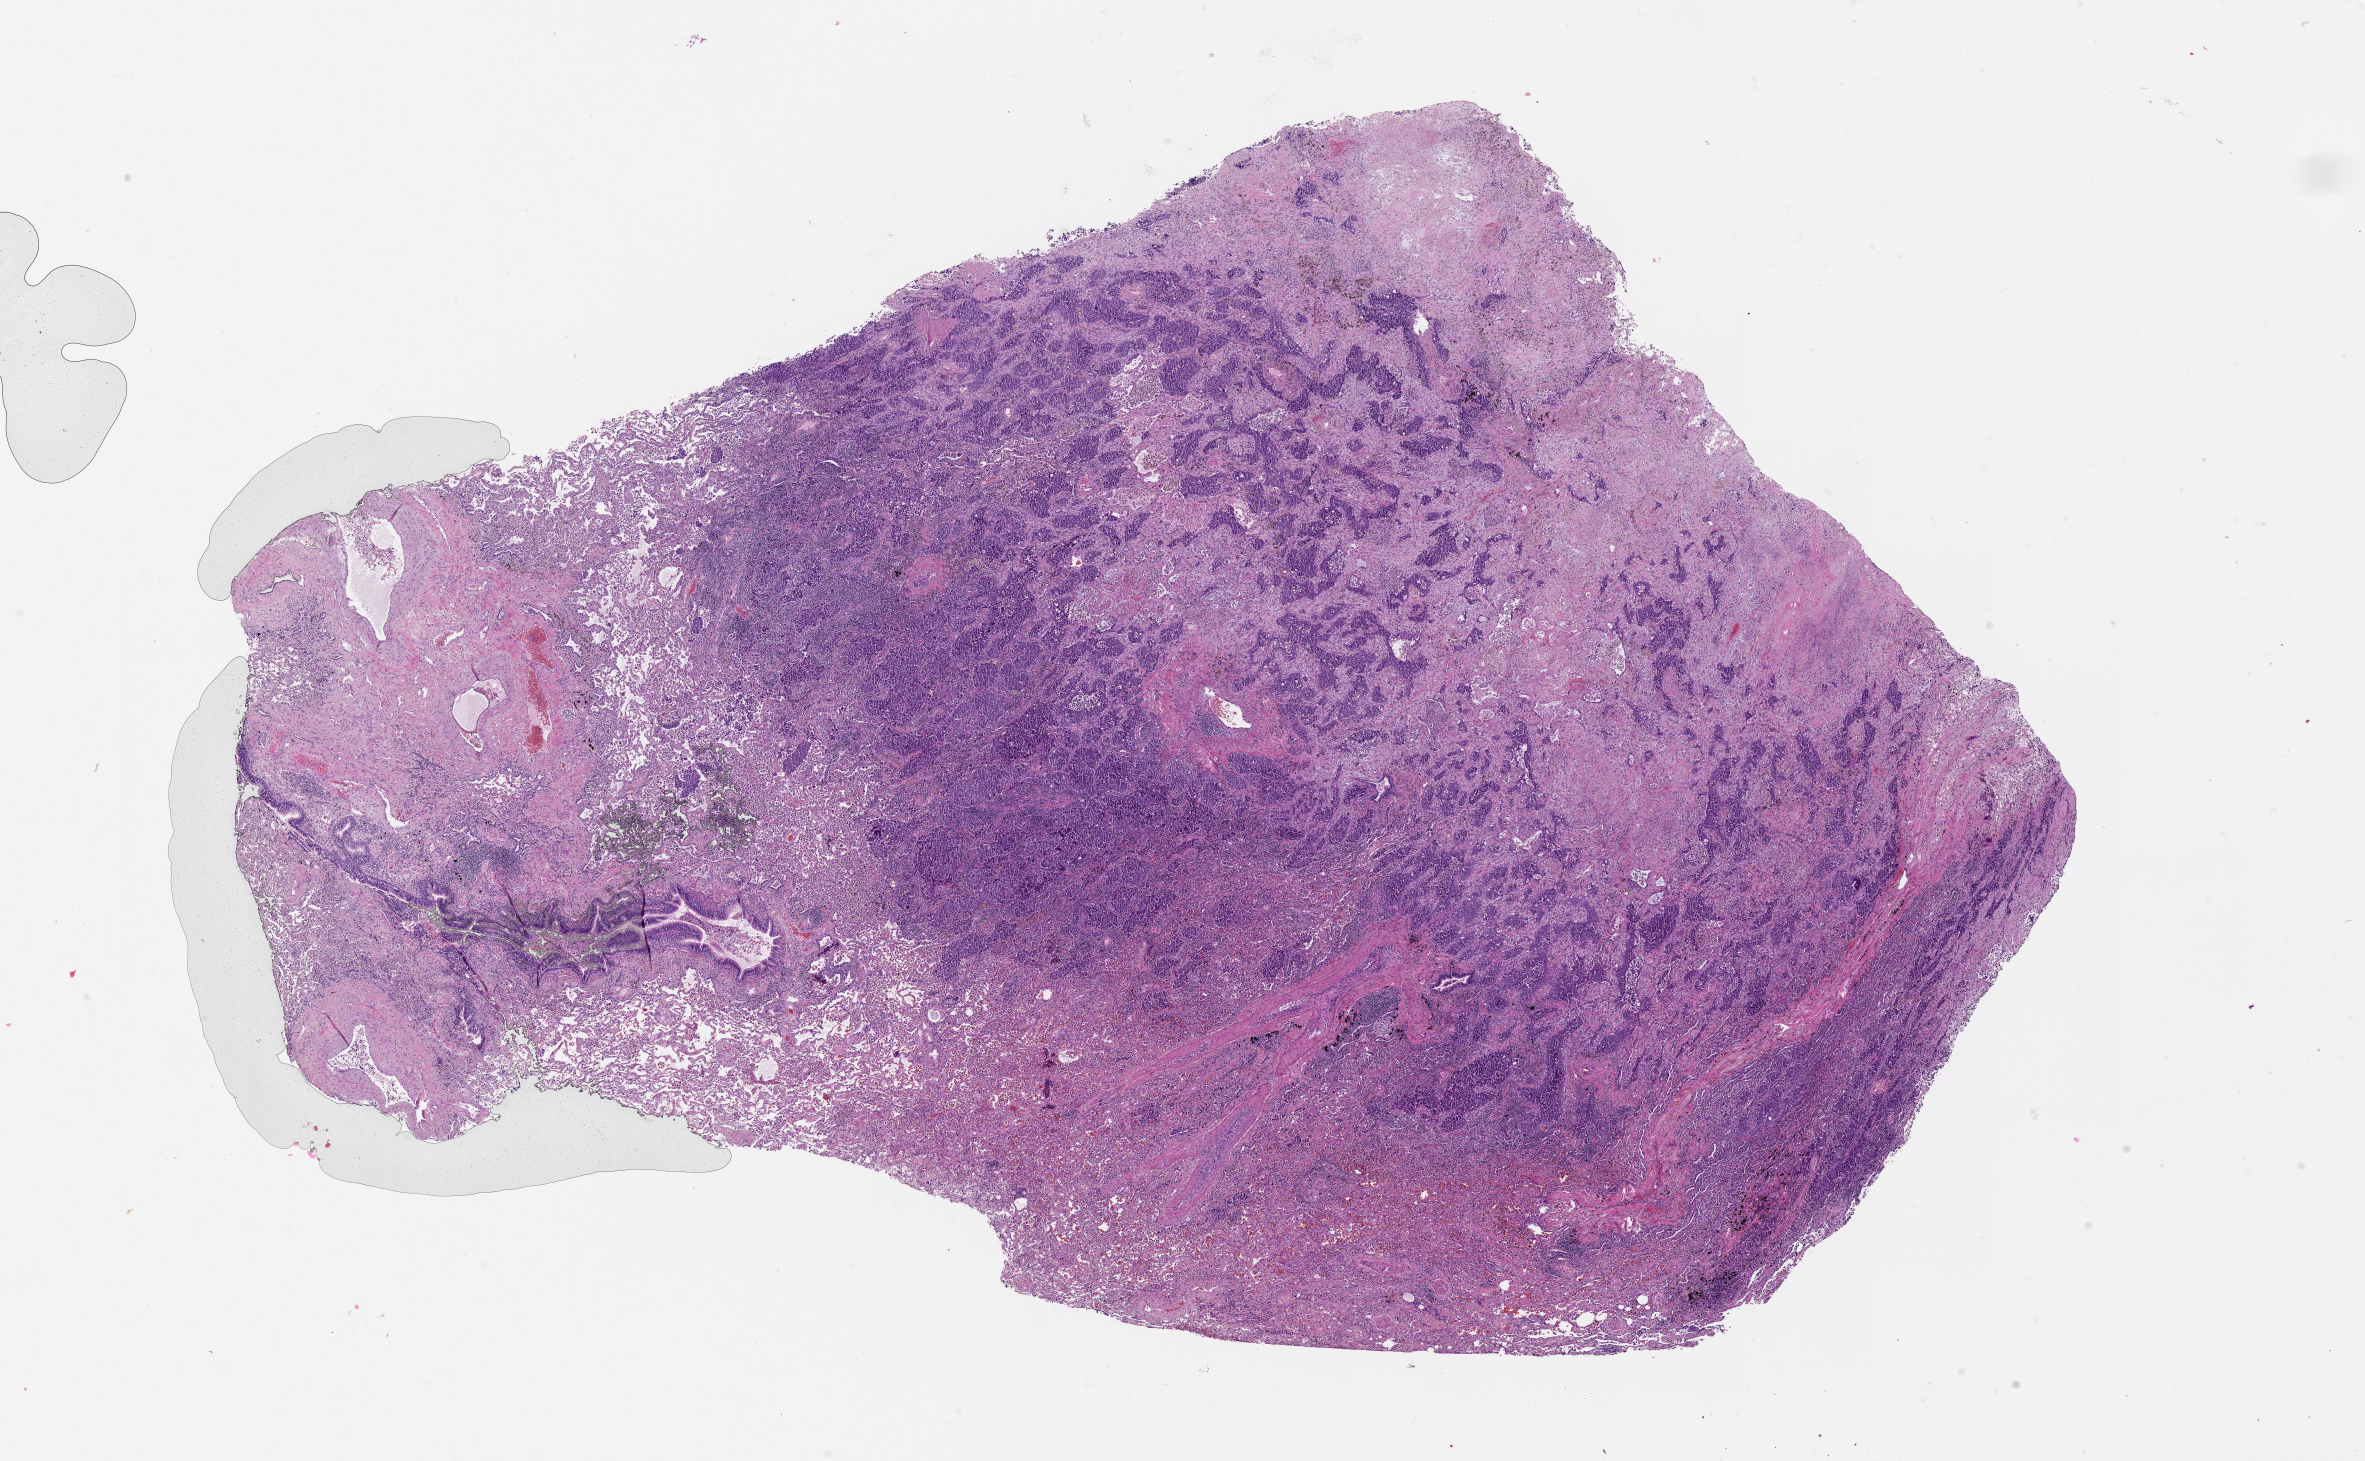
Whole-slide histology image, H&E-stained, shown as a low-resolution overview of the whole scanned area (about 19.0 x 11.8 mm, from a 20x scan). Lung, tumour tissue. 60-year-old male patient.
Patient diagnosis (cohort enrolment): squamous cell carcinoma (lung).